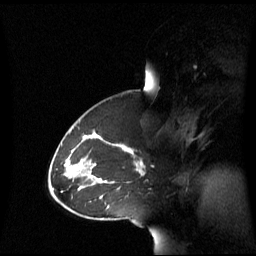
Breast MRI (dynamic contrast-enhanced), one sagittal slice. Position 40 of 60 along the scan axis. Dynamic contrast-enhanced series, image 2 of 3 at this slice position (ordered by acquisition). 1.5 T. TE 4.2 ms, TR 8.4 ms. 2.8 mm slice thickness. 256 × 256 image matrix. Female patient, age 43 years. Case-level facts recorded for this patient, not image findings: setting: breast cancer imaged before/during neoadjuvant chemotherapy; receptor status: triple-negative.
Outlined on this slice (semi-automatically segmented with operator editing):
- analysis volume of interest (the breast-tissue region the enhancement analysis was run in; not a lesion): bounding box <69,137,143,198> (left, top, right, bottom; pixels)
- tumour enhancement mask (voxels above the 70 % enhancement threshold inside the analysis volume of interest): <121,145,143,173>